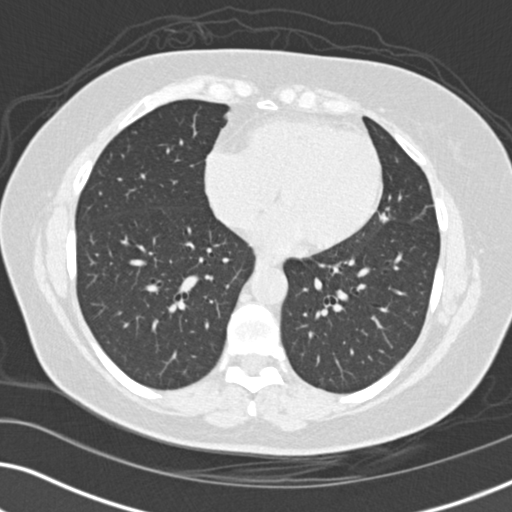
Low-dose screening chest CT, one axial slice; position 64 of 152 along the scan axis; 120 kVp; lung window (W 1500 / L -600 HU); 2 mm slice thickness; 512 × 512 image matrix, field of view 330 × 330 mm.
Outlined on this slice (outlined manually by an expert reader):
- lesion 1 (tumor, upper lobe of left lung): bounding box [x1, y1, x2, y2] px = [380, 211, 389, 224]